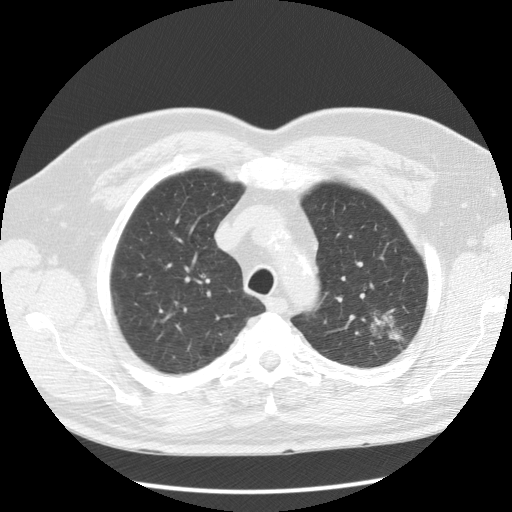
Axial slice from a low-dose chest CT screening exam; baseline screening round; lung window (W 1500 / L -600 HU); 2.5 mm slice thickness; standard (soft-tissue) reconstruction kernel (STANDARD); 512 × 512 image matrix. Male participant, aged 60 years at enrolment. Current smoker at enrolment.
Expert-annotated lung lesion, bounding box <359,299,418,362> (left, top, right, bottom; pixels). The screening reader recorded 3 non-calcified nodules or masses ≥4 mm on this exam (left upper lobe, right upper lobe, left upper lobe); which of them this box marks is not recorded. Official screen result: positive, change unspecified: nodule(s) >= 4 mm or enlarging nodule(s), mass(es), or other non-specific abnormalities suspicious for lung cancer. Lung cancer was diagnosed 48 days after this screen: bronchiolo-alveolar adenocarcinoma, NOS, left upper lobe, well differentiated (G1), stage IA (AJCC 6th edition), 27 mm at pathology.